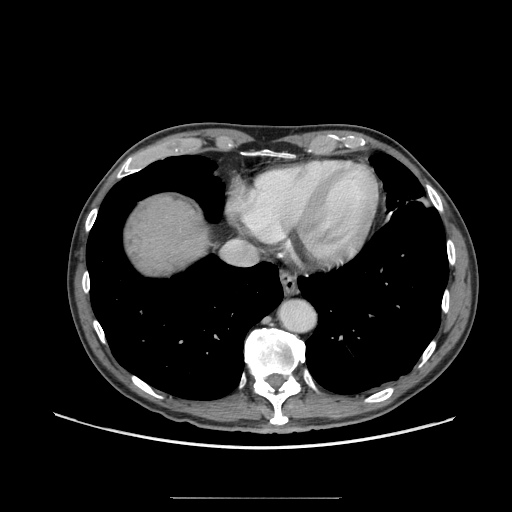
Contrast-enhanced abdominal CT (liver protocol), one axial slice. Position 64 of 71 along the scan axis. Reconstruction kernel STANDARD. Soft-tissue window (W 400 / L 40 HU). 2.5 mm slice thickness. 512 × 512 image matrix, field of view 400 × 400 mm. From the clinical record (not read from this slice): diagnosis: hepatocellular carcinoma (patient treated with transarterial chemoembolisation; whether this scan precedes or follows treatment is not stated here); TNM stage (as recorded): Stage-I; Child-Pugh class: A; tumour nodularity: uninodular; tumour size: 3.5 cm.
Structures marked on this image (semi-automatically segmented with operator editing):
- abdominal aorta: box from (x=280, y=300) to (x=315, y=332) px
- liver parenchyma outside the tumour (the mass and vessels are separate outlines, so this box may not span the whole liver): (x=131, y=198)–(x=208, y=272)